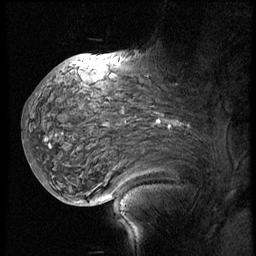
Breast MRI (dynamic contrast-enhanced), one sagittal slice. 3 images stored at this slice position (order not interpretable as contrast timing). 1.5 T. TE 4.2 ms, TR 8.9 ms. 2.5 mm slice thickness. 256 × 256 image matrix, field of view 200 × 200 mm. Patient: female, 57 years. Case-level facts recorded for this patient, not image findings: setting: breast cancer imaged before/during neoadjuvant chemotherapy; receptor status: HER2-positive.
Structures marked on this image (semi-automatic segmentation, software-assisted and operator-edited):
- analysis volume of interest (the breast-tissue region the enhancement analysis was run in; not a lesion): box from (x=34, y=75) to (x=214, y=171) px
- tumour enhancement mask (voxels above the 140 % enhancement threshold inside the analysis volume of interest): (x=47, y=120)–(x=161, y=141)